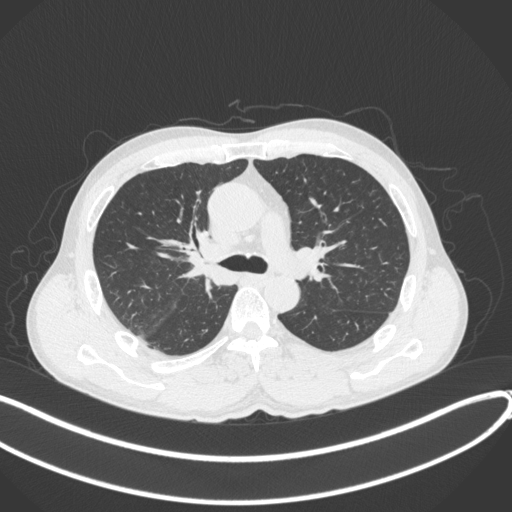
Chest CT, one axial slice. Slice 248 of 409 in the series (ordered by position). Reconstruction kernel B31f. Lung window (W 1500 / L -600 HU). 1 mm slice thickness. 512 × 512 image matrix. Male patient, age 53 years. Case-level facts recorded for this patient, not image findings: clinical TNM (as recorded): T1b N0 M0.
Annotated regions visible in this slice (bounding box drawn by a radiologist):
- lung tumour (recorded histology: squamous cell carcinoma): box from (x=183, y=229) to (x=237, y=293) px